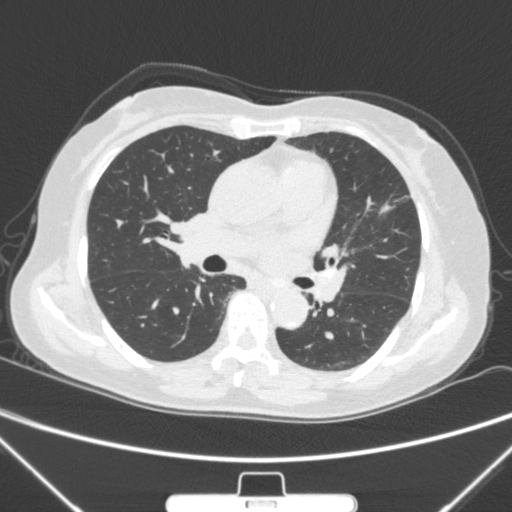
Chest CT, one axial slice. Slice 153 of 300 in the series (ordered by position). Lung window (W 1500 / L -600 HU). 1 mm slice thickness. 512 × 512 image matrix, field of view 350 × 350 mm. Patient: female, 70 years. From the clinical record (not read from this slice): clinical TNM (as recorded): T1b N0 M0.
Structures marked on this image (bounding box drawn by a radiologist):
- lung tumour (recorded histology: adenocarcinoma): box from (x=368, y=190) to (x=396, y=226) px